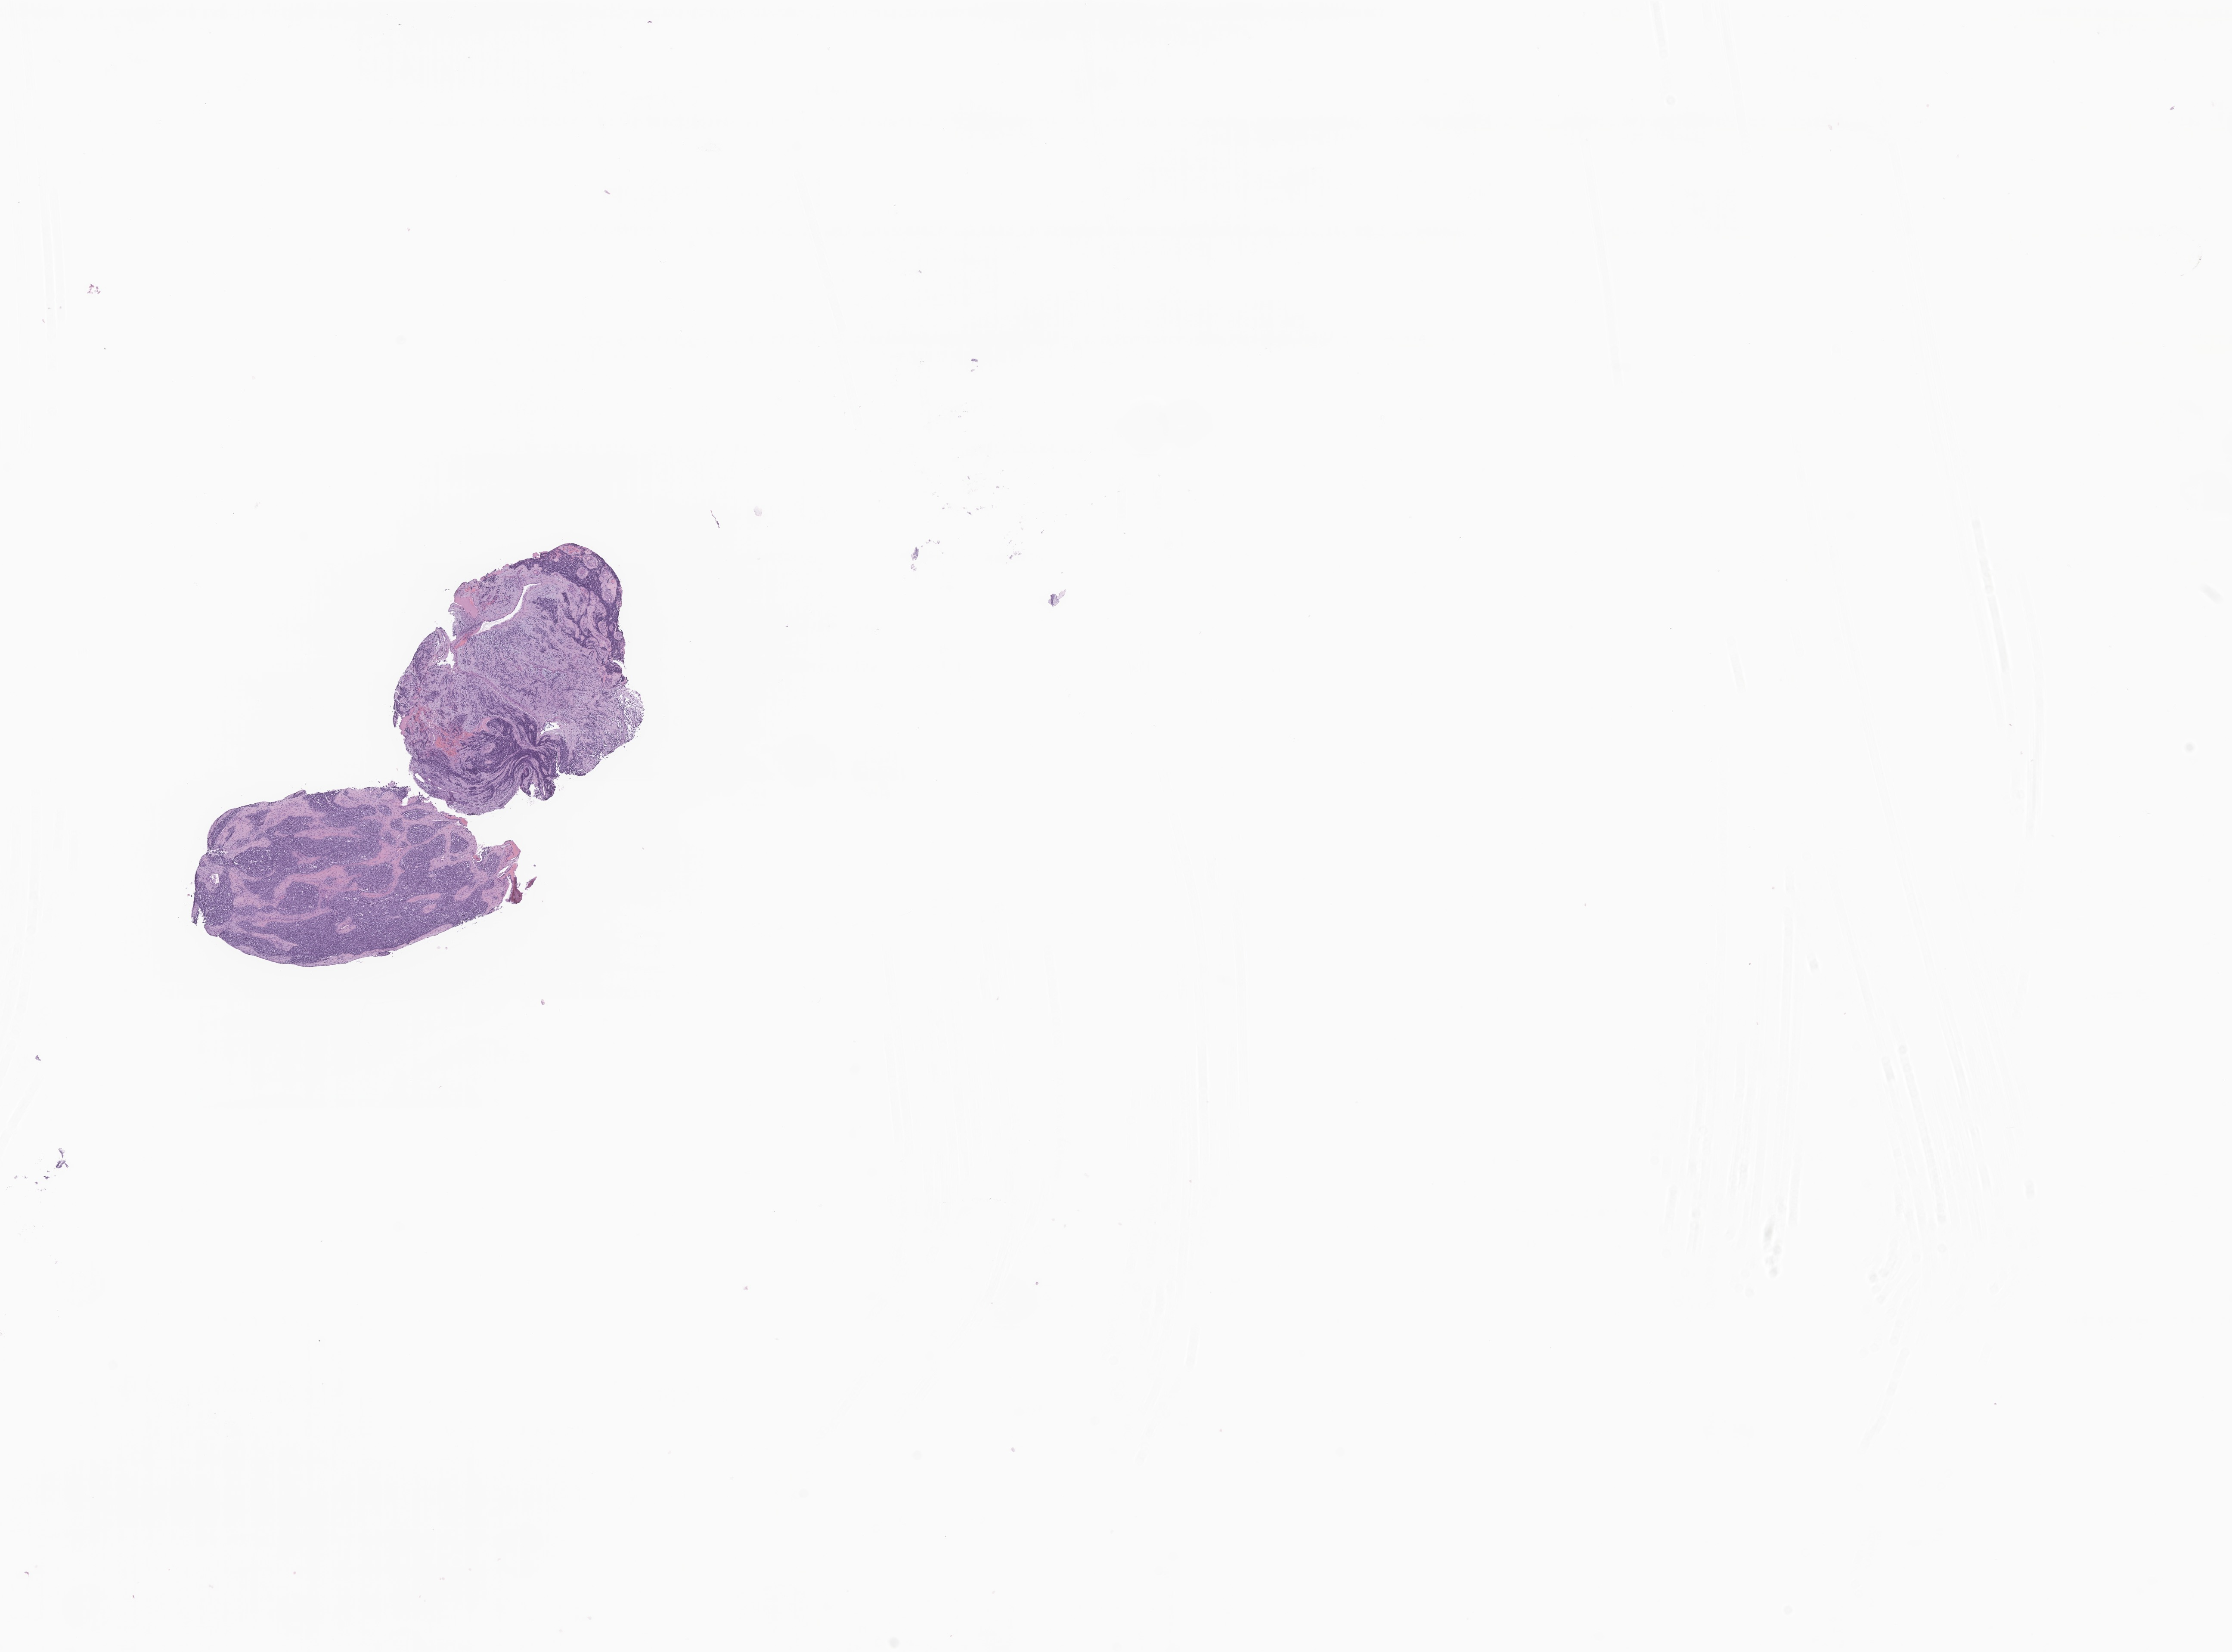
Hematoxylin and eosin (H&E) whole-slide image of tumor tissue from the sphenoid sinus, shown as a low-resolution overview of the whole scanned area (about 21.9 x 16.2 mm); formalin-fixed paraffin-embedded section. Patient male; age 105 months (8 years 9 months).
Diagnosis: Rhabdomyosarcoma, NOS.